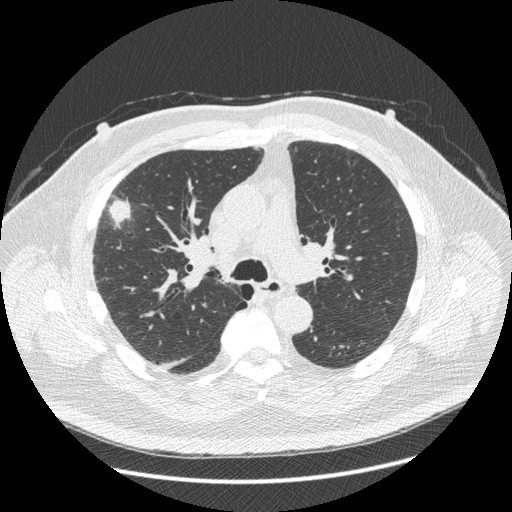
Chest CT (low-dose screening protocol), one axial image, third screening round (two years after baseline), lung window (W 1500 / L -600 HU), 1.25 mm slice thickness, 120 kVp. Male, age 66 years at enrolment.
- Expert reader's lesion annotation, box from (x=86, y=179) to (x=145, y=264) px.
- The exam's reader record, not a measurement of the box and not confirmed to be the same lesion: non-calcified nodule or mass ≥4 mm, right upper lobe, 48 × 25 mm, spiculated (stellate) margins, soft tissue attenuation, pre-existing on the prior screen: no.
- Official screen result: positive, other.
- Lung cancer was diagnosed 35 days after this screen: non-small cell carcinoma, right upper lobe, stage IV (AJCC 6th edition), 50 mm at pathology.